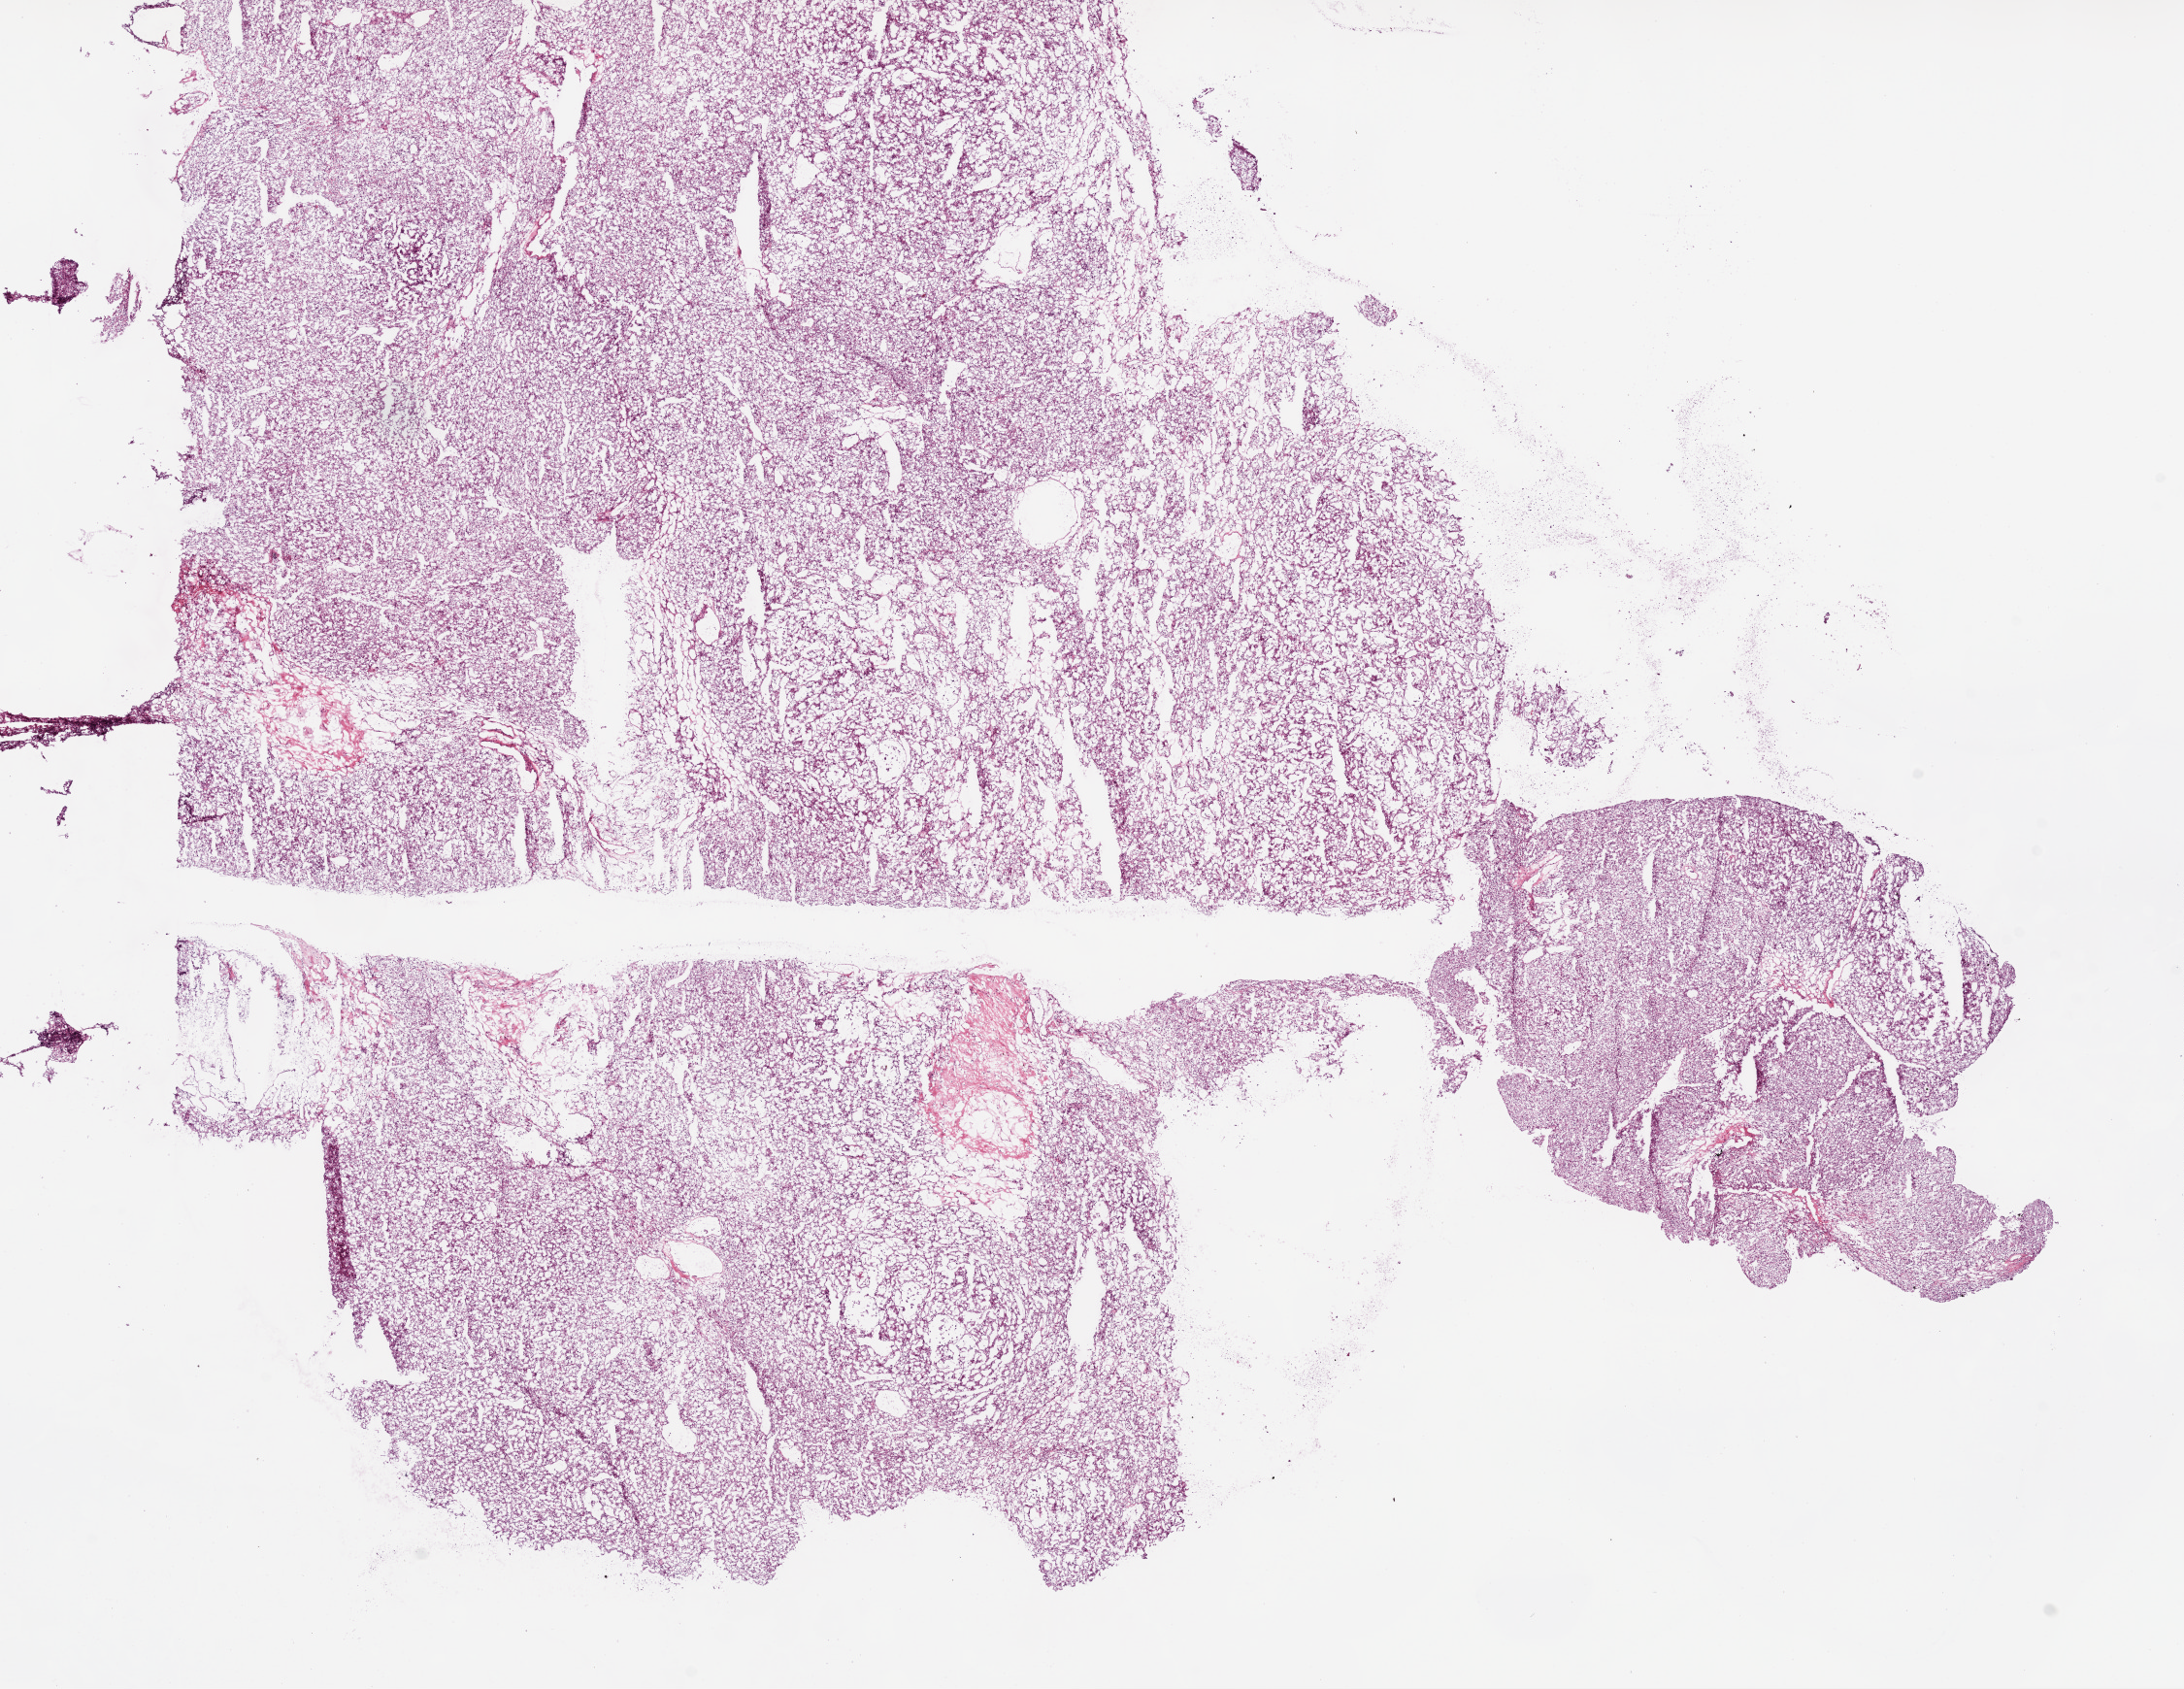
Digitized H&E tissue section (whole slide), whole scanned area (about 18.1 x 14.0 mm, acquisition: 20x scan) shown as a low-resolution overview, frozen section, kidney, primary tumour sample. Female, age 76 years at initial diagnosis. Histologic grade: G3 (poorly differentiated). Pathologist review of this section (percent, as recorded): tumour cells 95%, tumour nuclei 85%, normal cells 0%, stromal cells 5%, necrosis 0%.
Histologic diagnosis: Clear cell adenocarcinoma, NOS. Laterality: left. TNM: T3a N0 M0. AJCC pathologic stage: III.